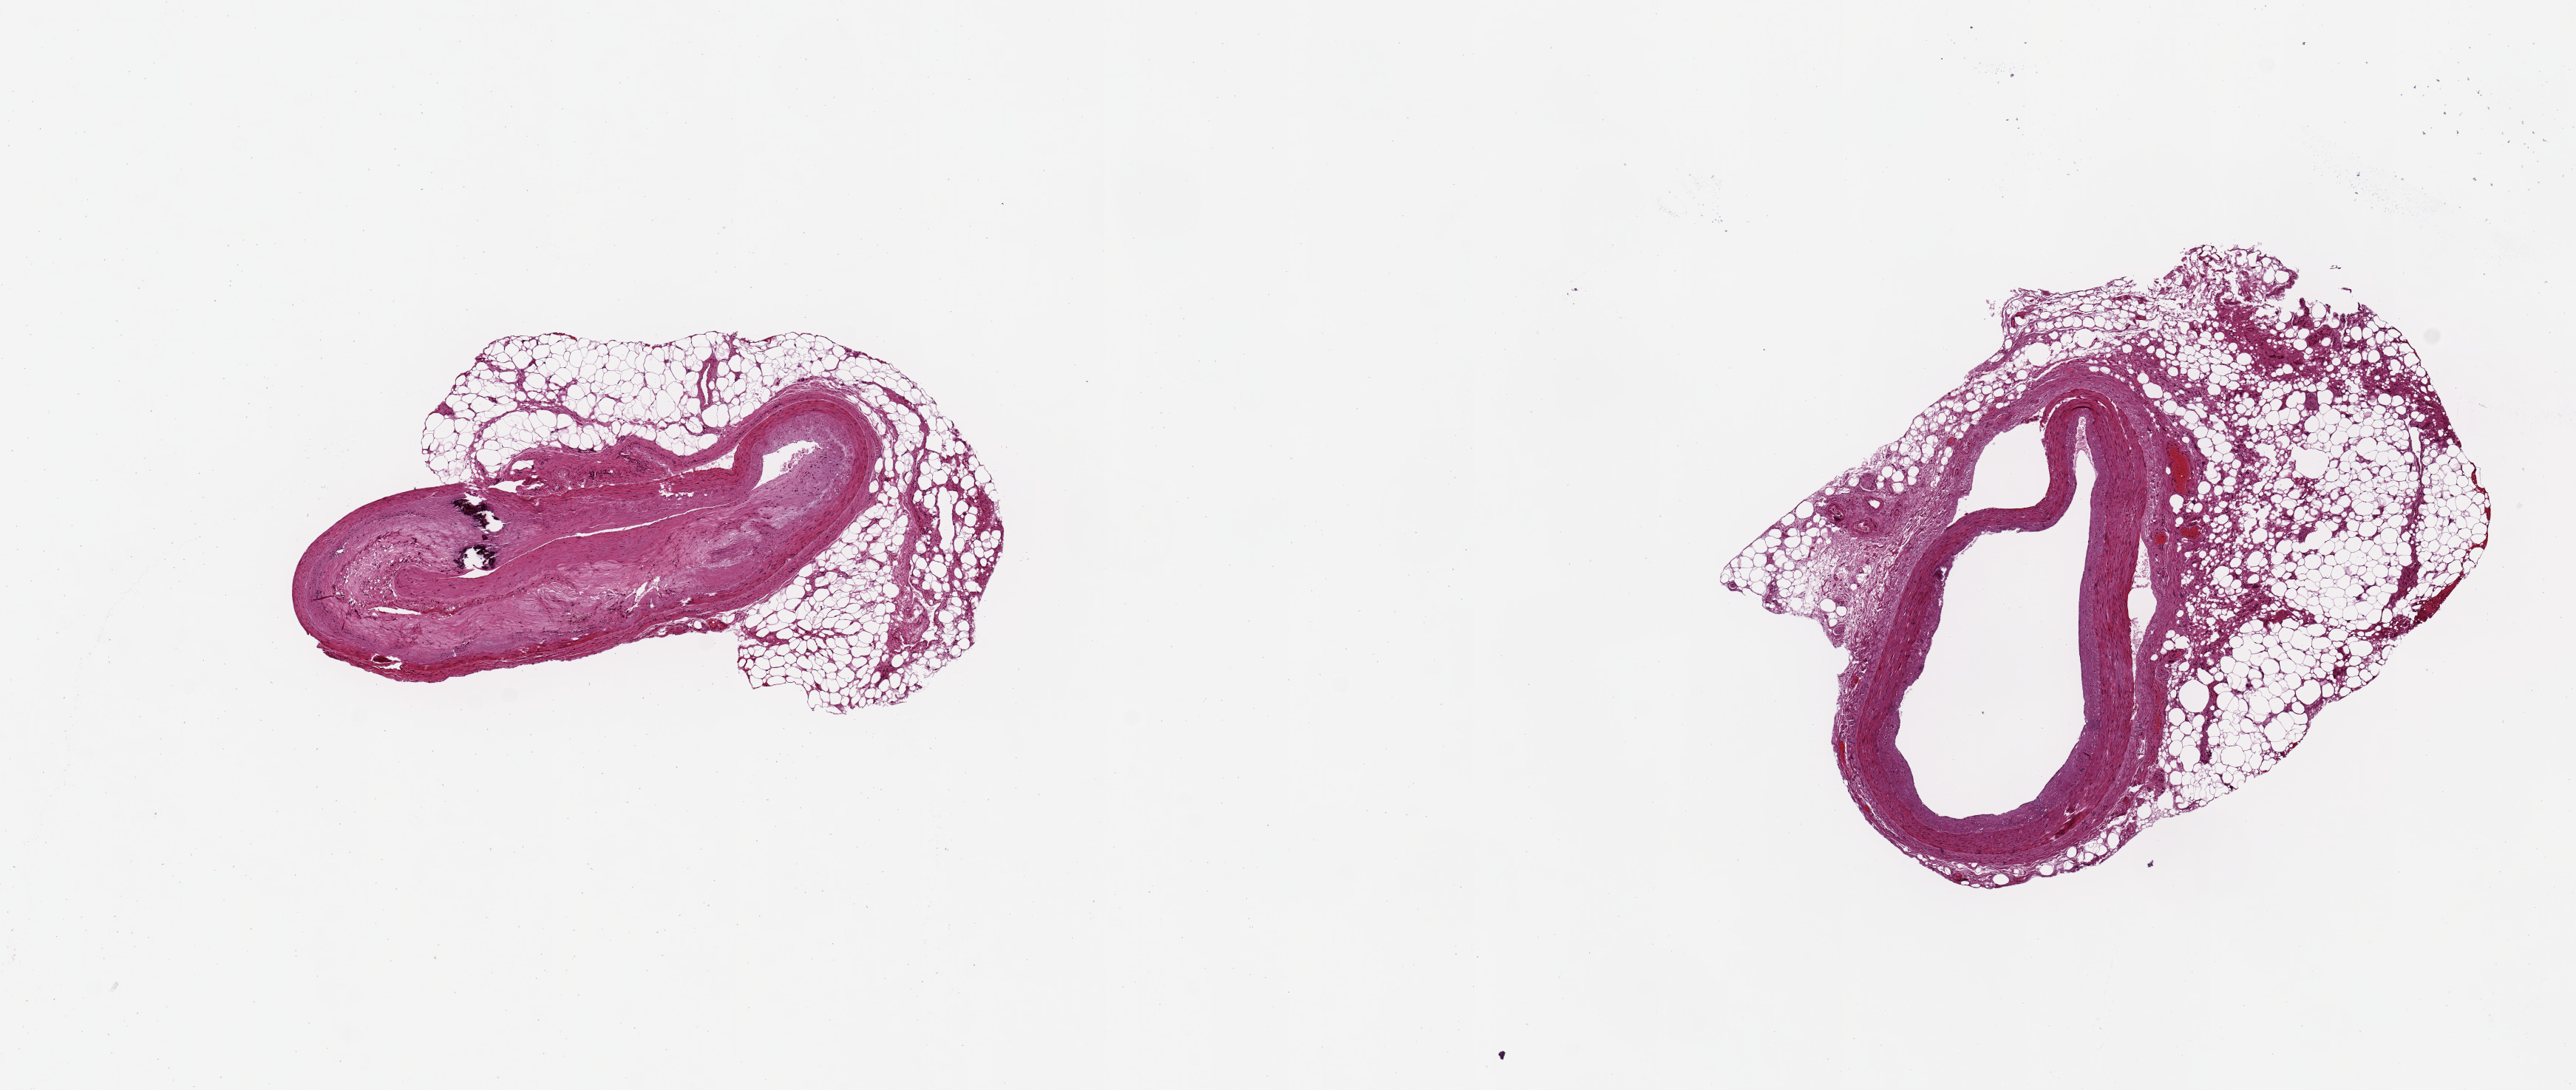
Whole-slide image, haematoxylin and eosin stain, low-resolution overview of the scanned area, about 13.8 x 5.8 mm, PAXgene-fixed paraffin-embedded (PFPE) section, section of coronary artery (target tissue), tissue donor sample.
* reviewer comment on this tissue sample: 2 arteries ~3mm in diameter, one with moderate atherosclerosis; both have 40-60% adjacent adipose tissue